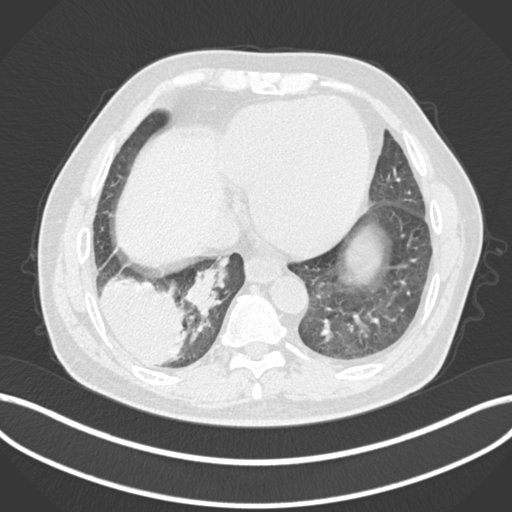
Chest CT, one axial slice; position 38 of 200 along the scan axis; lung window (W 1500 / L -600 HU); 1 mm slice thickness; 512 × 512 image matrix, field of view 400 × 400 mm. Patient: male, 59 years.
Outlined on this slice (bounding box drawn by a radiologist):
- lung tumour (recorded histology: adenocarcinoma): bounding box <93,276,190,368> (left, top, right, bottom; pixels)